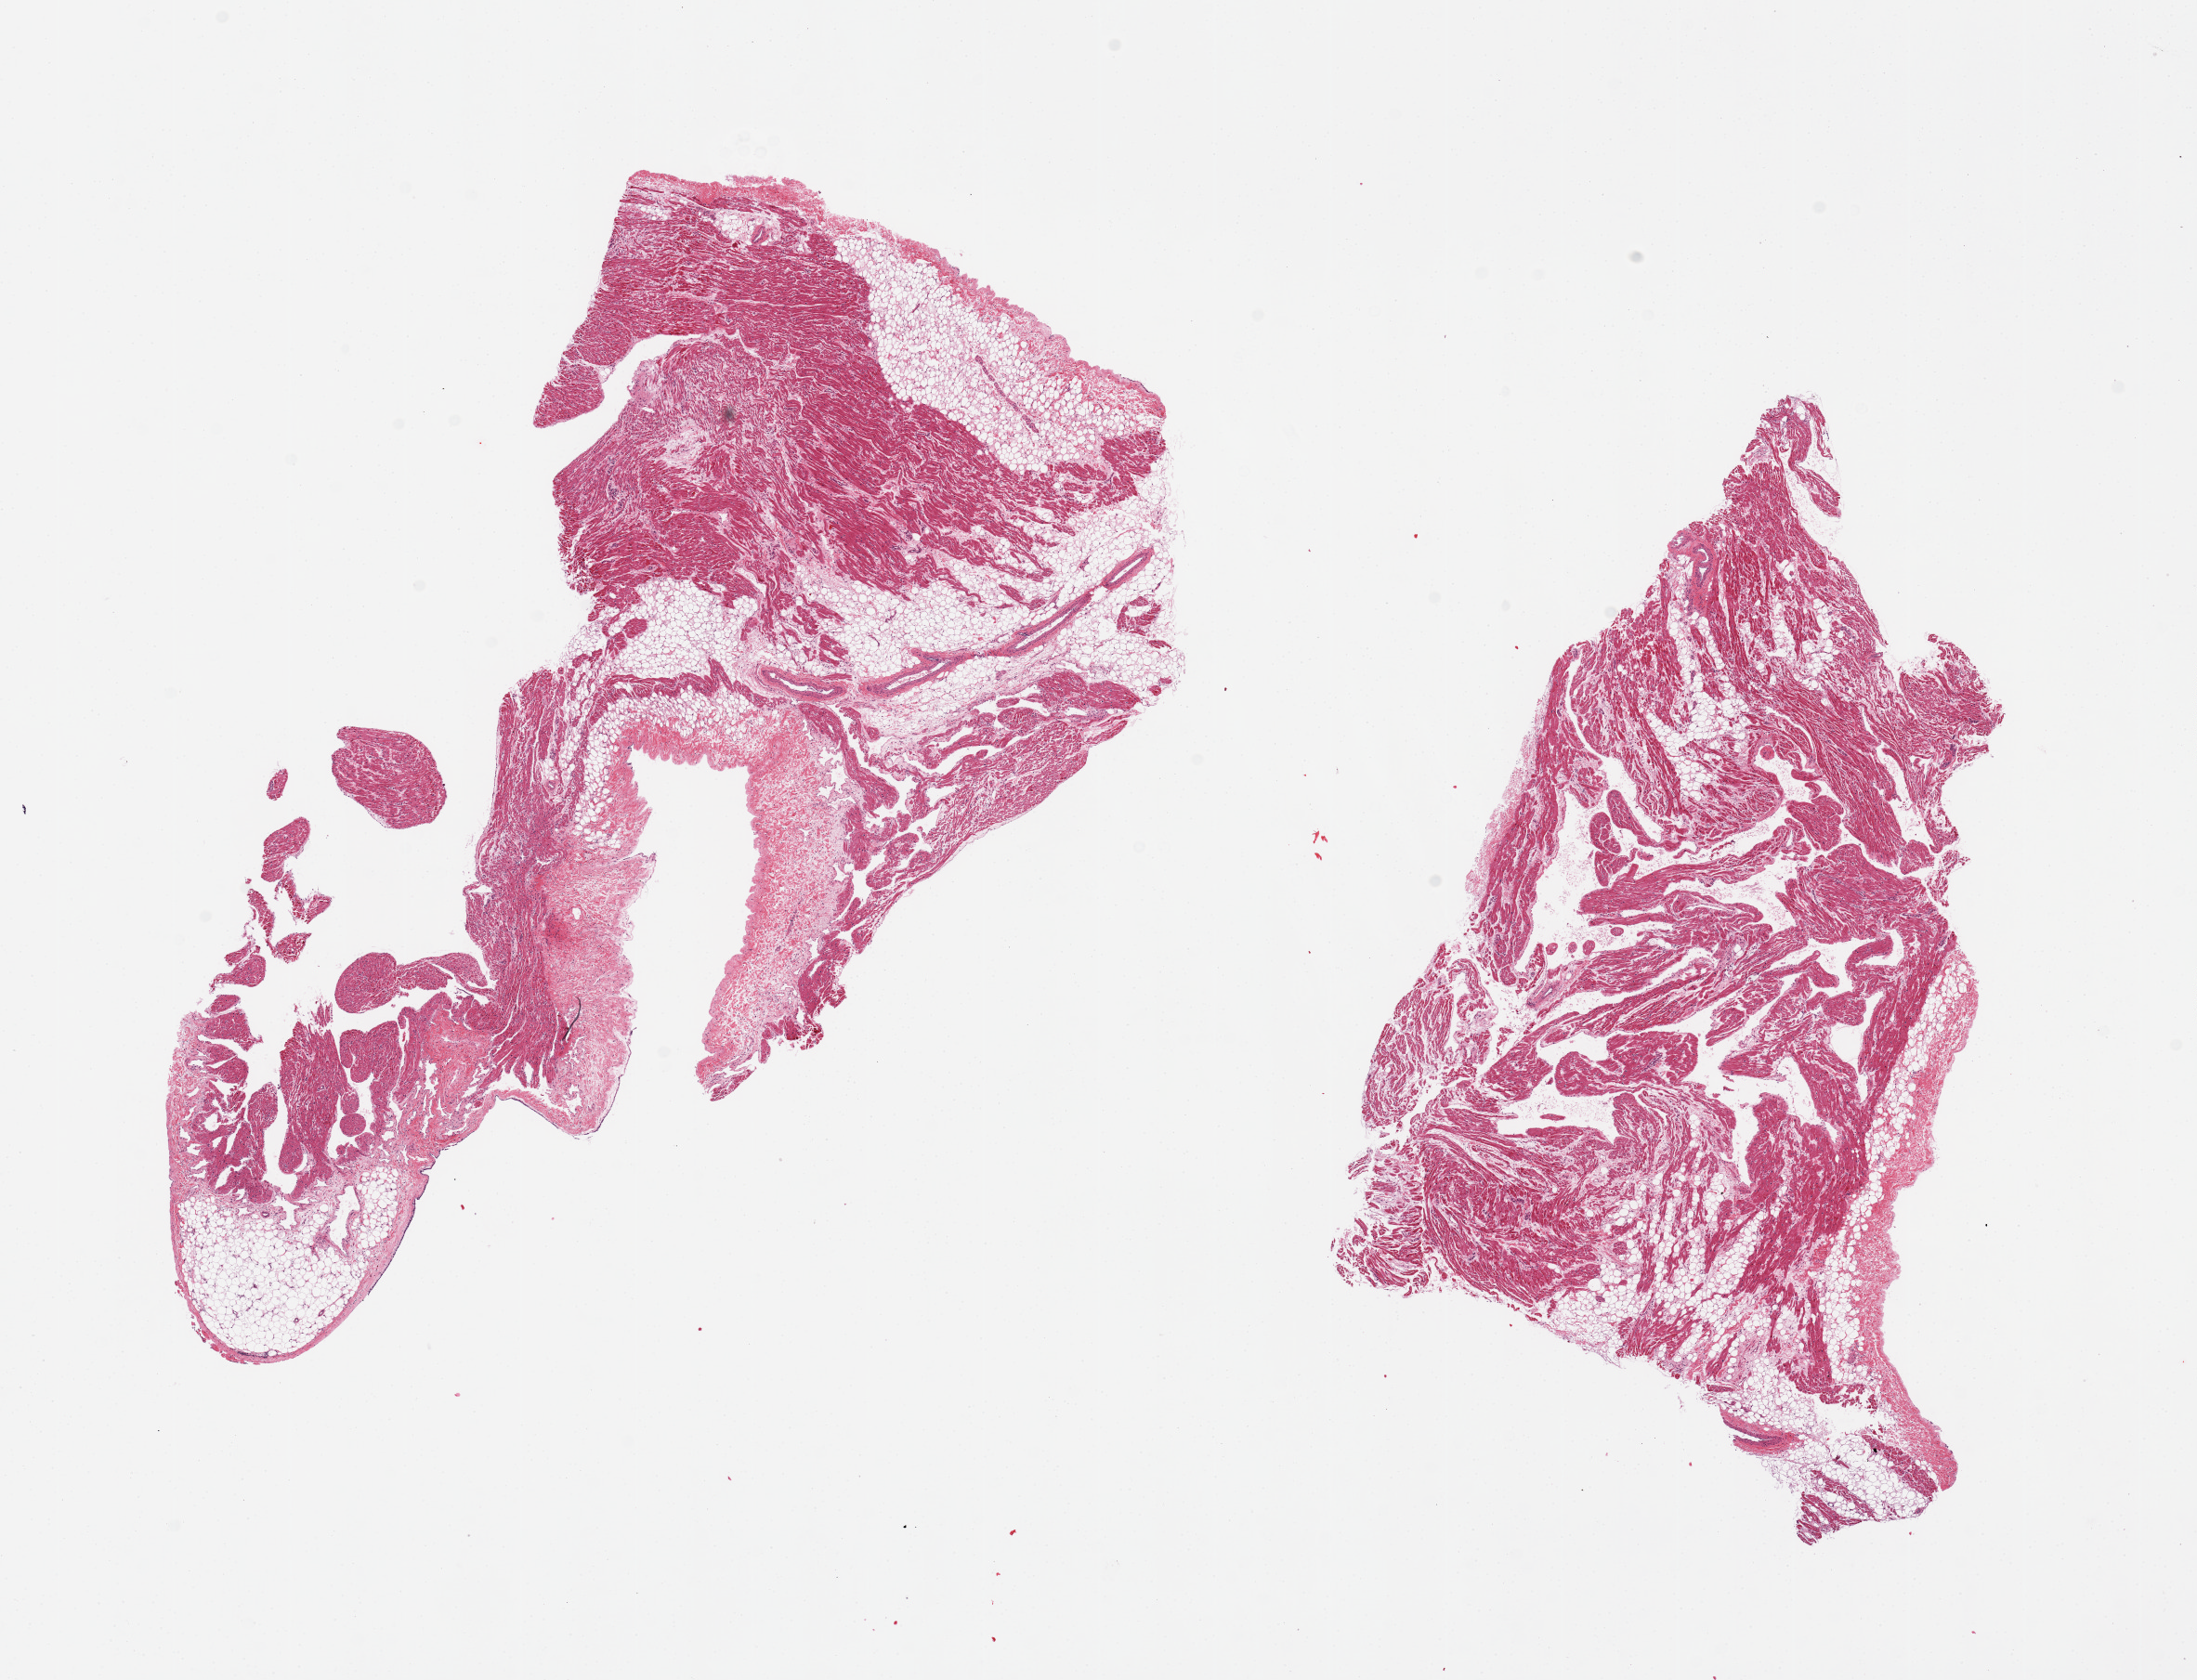
Whole-slide image, haematoxylin and eosin stain, whole scanned area (about 18.7 x 14.3 mm) shown as a low-resolution overview; PAXgene-fixed paraffin-embedded (PFPE) section; target tissue: auricular appendage; donor tissue sample. Donor sex: female.
Reviewer comment on this tissue sample: 2 pieces, 30-40% fat.